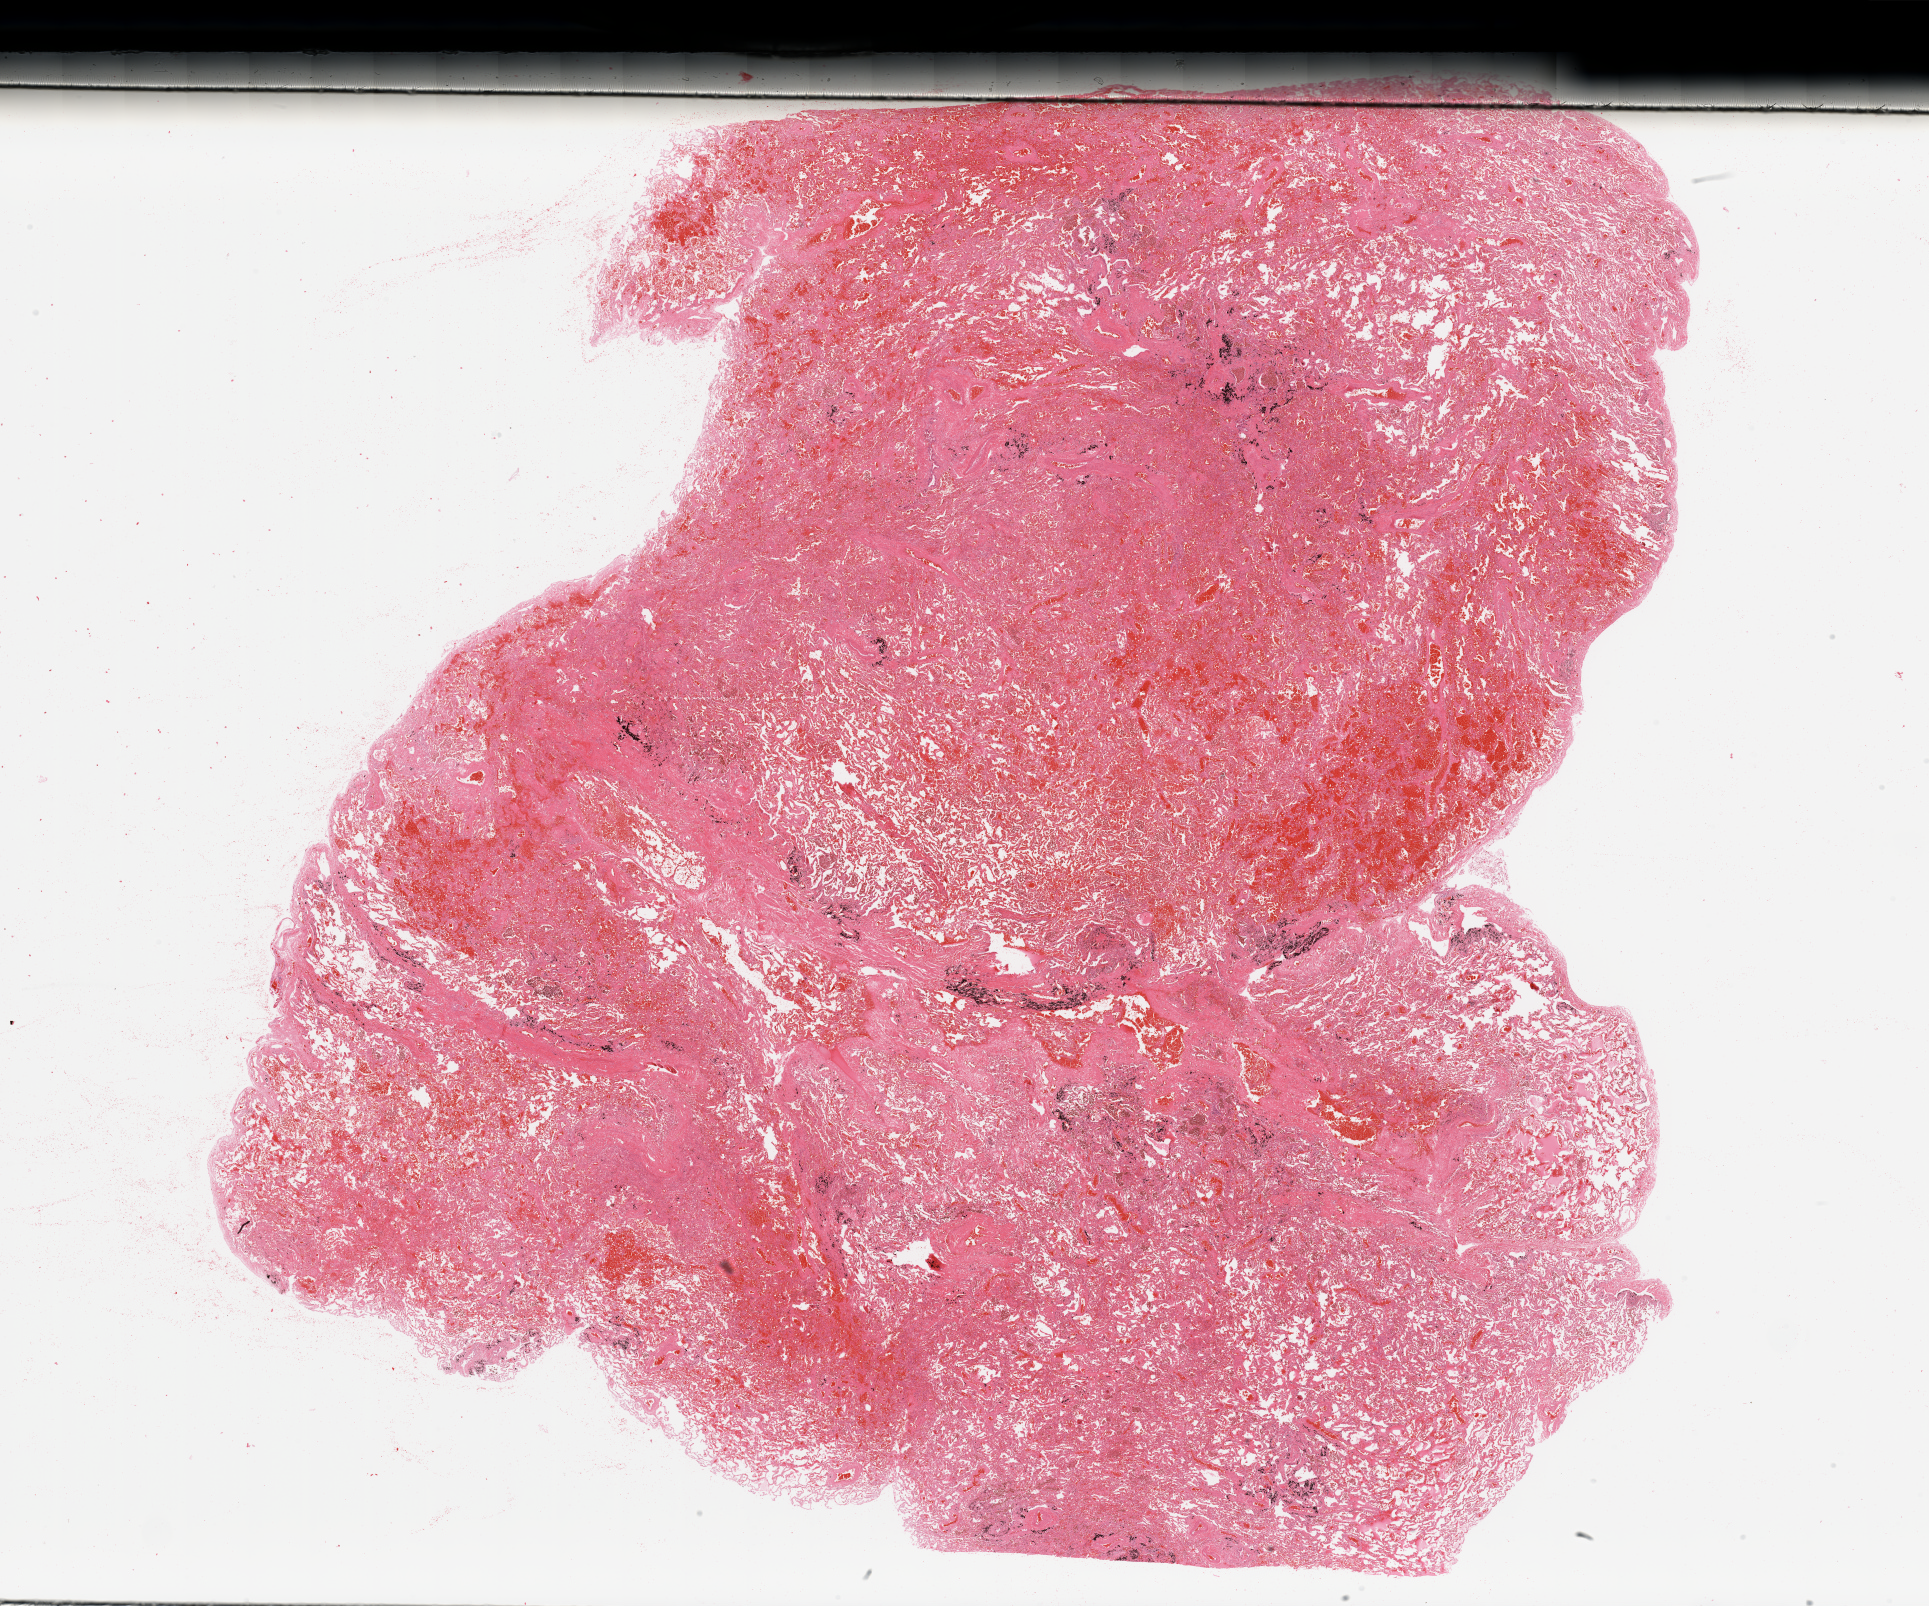
Whole-slide histology image, Hematoxylin and eosin (H&E) stained, whole scanned area (about 30.5 x 25.4 mm) shown as a low-resolution overview. Lung, normal (non-tumour) tissue. Male, 59 y/o.
This section: normal (non-tumour) tissue from the same patient. Patient diagnosis: Adenocarcinoma, NOS.